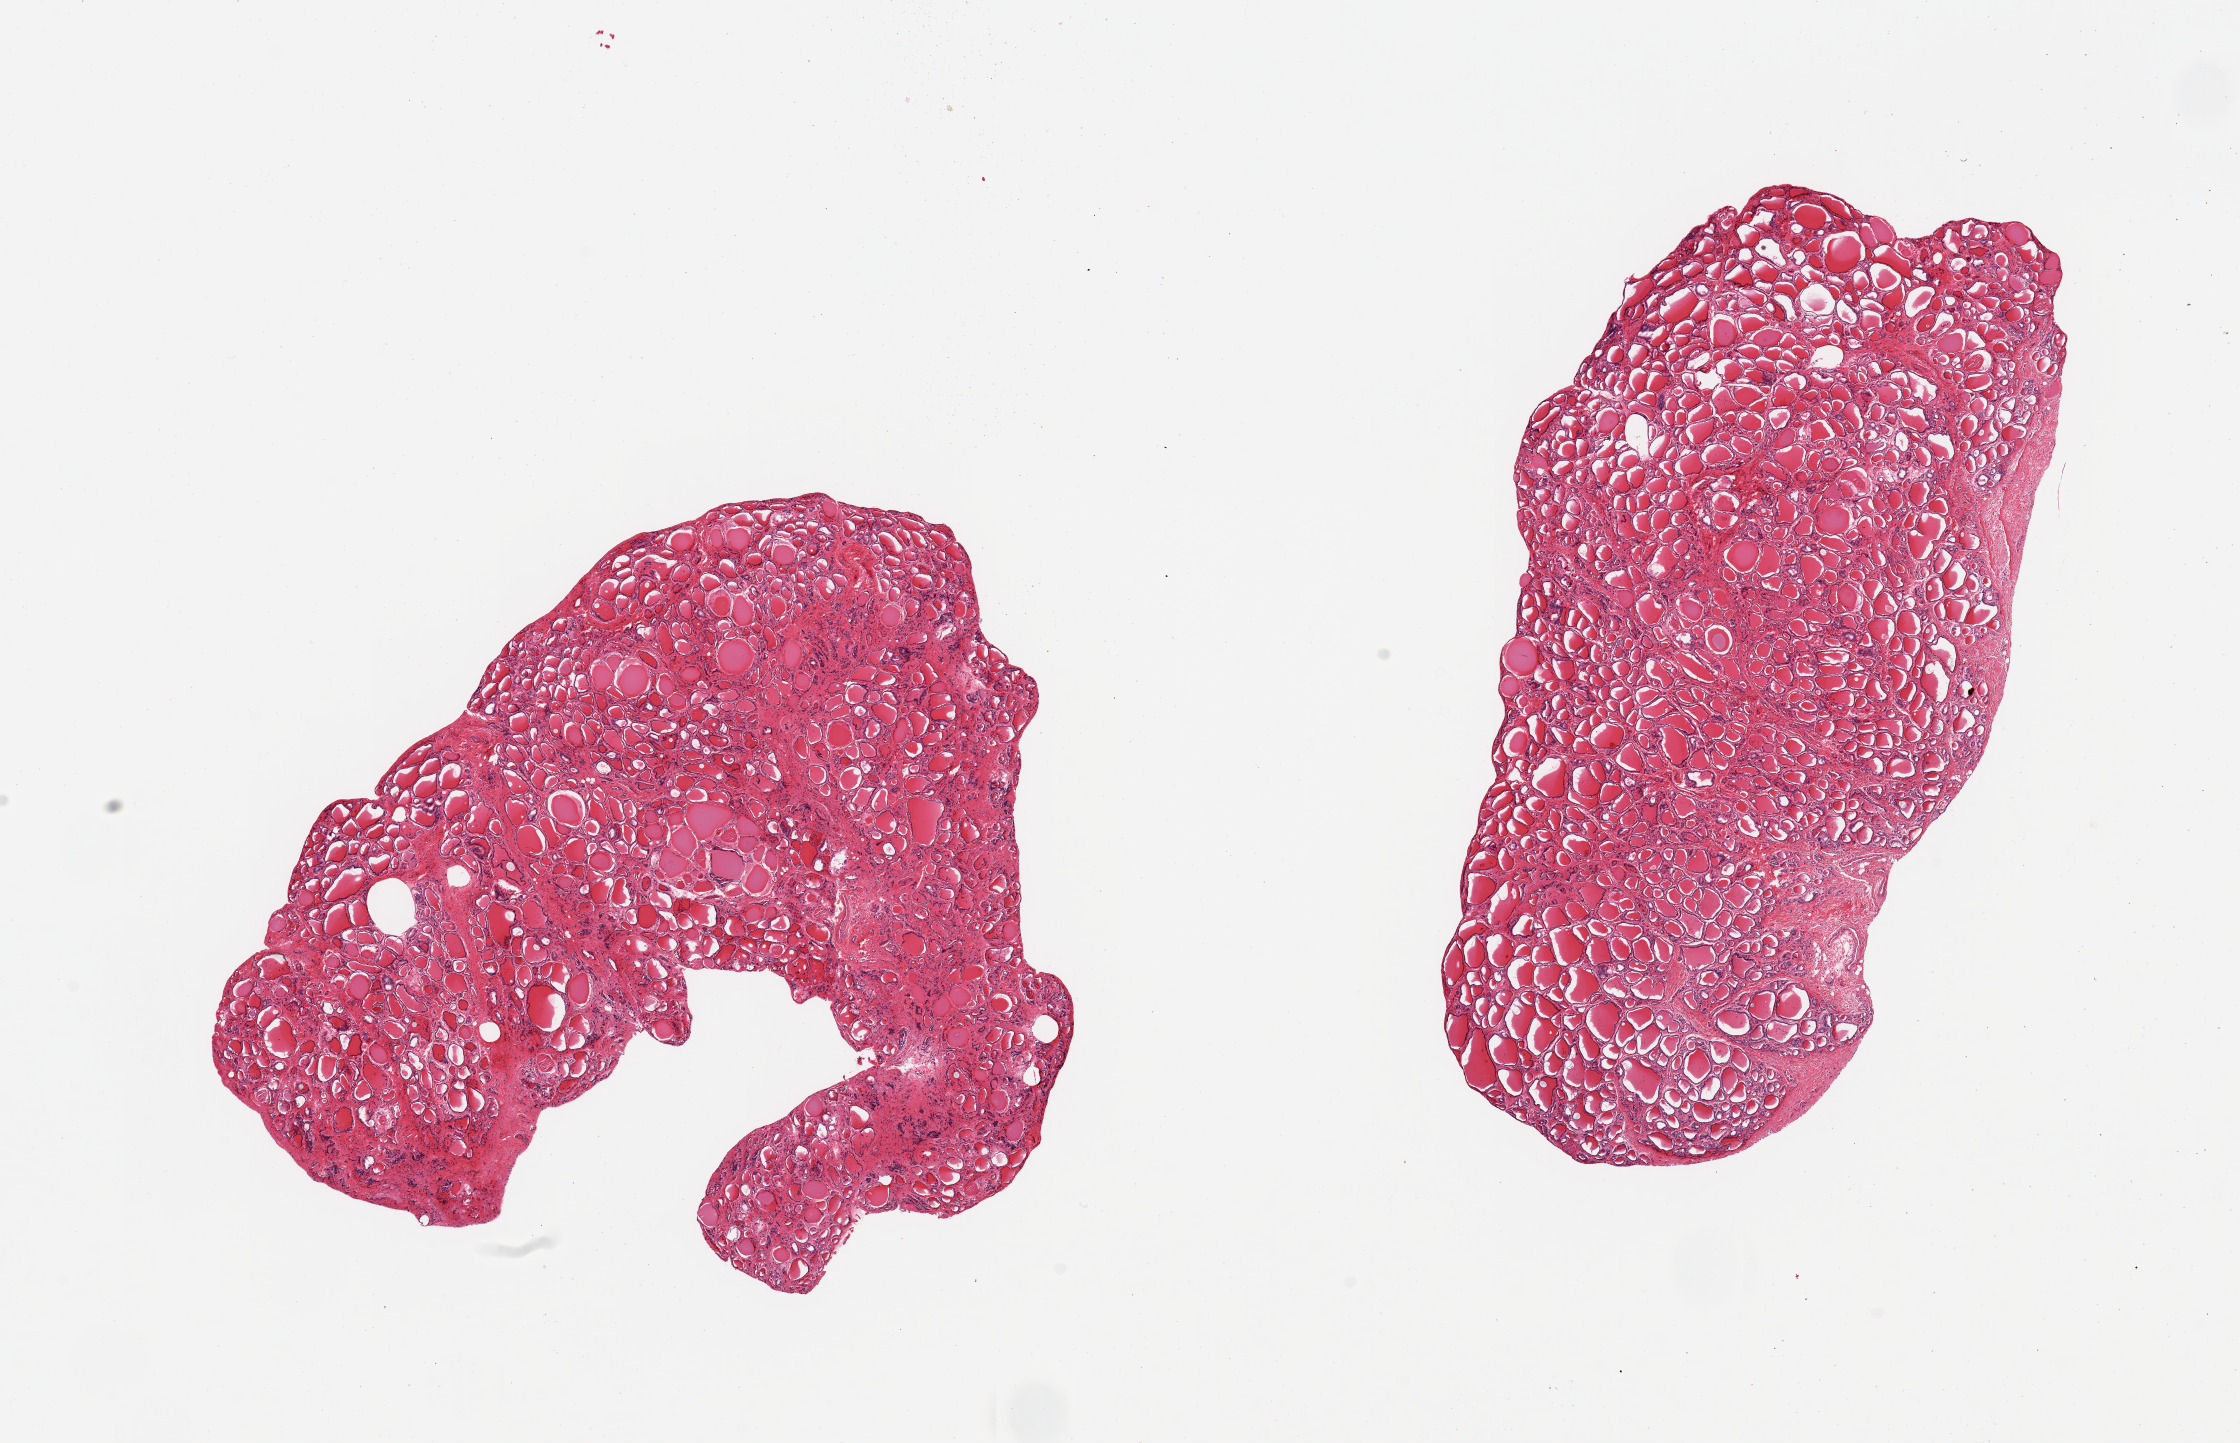
Hematoxylin and eosin (H&E) whole-slide image, brightfield — whole scanned area (about 17.7 x 11.4 mm) shown as a low-resolution overview. PAXgene-fixed paraffin-embedded (PFPE) section. Sampled site (target tissue): thyroid. Donor tissue sample. Donor sex: female.
• pathologist's review note for this sample: 2 pieces